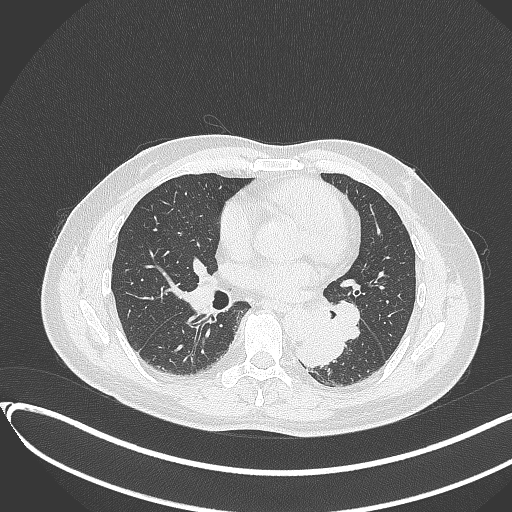
Chest CT, one axial slice. Slice 169 of 417 in the series (ordered by position). Reconstruction kernel B70f. 120 kVp. Lung window (W 1500 / L -600 HU). 1 mm slice thickness. 512 × 512 image matrix, field of view 400 × 400 mm. Patient: male, 54 years. Case-level facts recorded for this patient, not image findings: clinical TNM (as recorded): T3 N0 M0.
Outlined on this slice (bounding box drawn by a radiologist):
- lung tumour (recorded histology: squamous cell carcinoma): bounding box <290,325,348,371> (left, top, right, bottom; pixels)